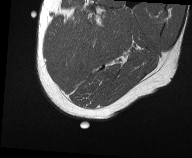
MRI of an extremity soft-tissue mass, one axial slice; slice 6 of 61 in the series (ordered by position); MR volume resampled by the dataset authors to the PET/CT grid (not the native acquisition matrix); 3.27 mm slice thickness; 192 × 158 image matrix, field of view 187 × 154 mm. Male patient. Case-level facts recorded for this patient, not image findings: histological type: pleiomorphic liposarcoma; grade: high; site of the primary tumour: left thigh.
Annotated regions visible in this slice (expert contour drawn on MRI and transferred to this co-registered scan by the dataset authors):
- gross tumour volume including surrounding oedema: bounding box <75,16,110,36> (left, top, right, bottom; pixels)